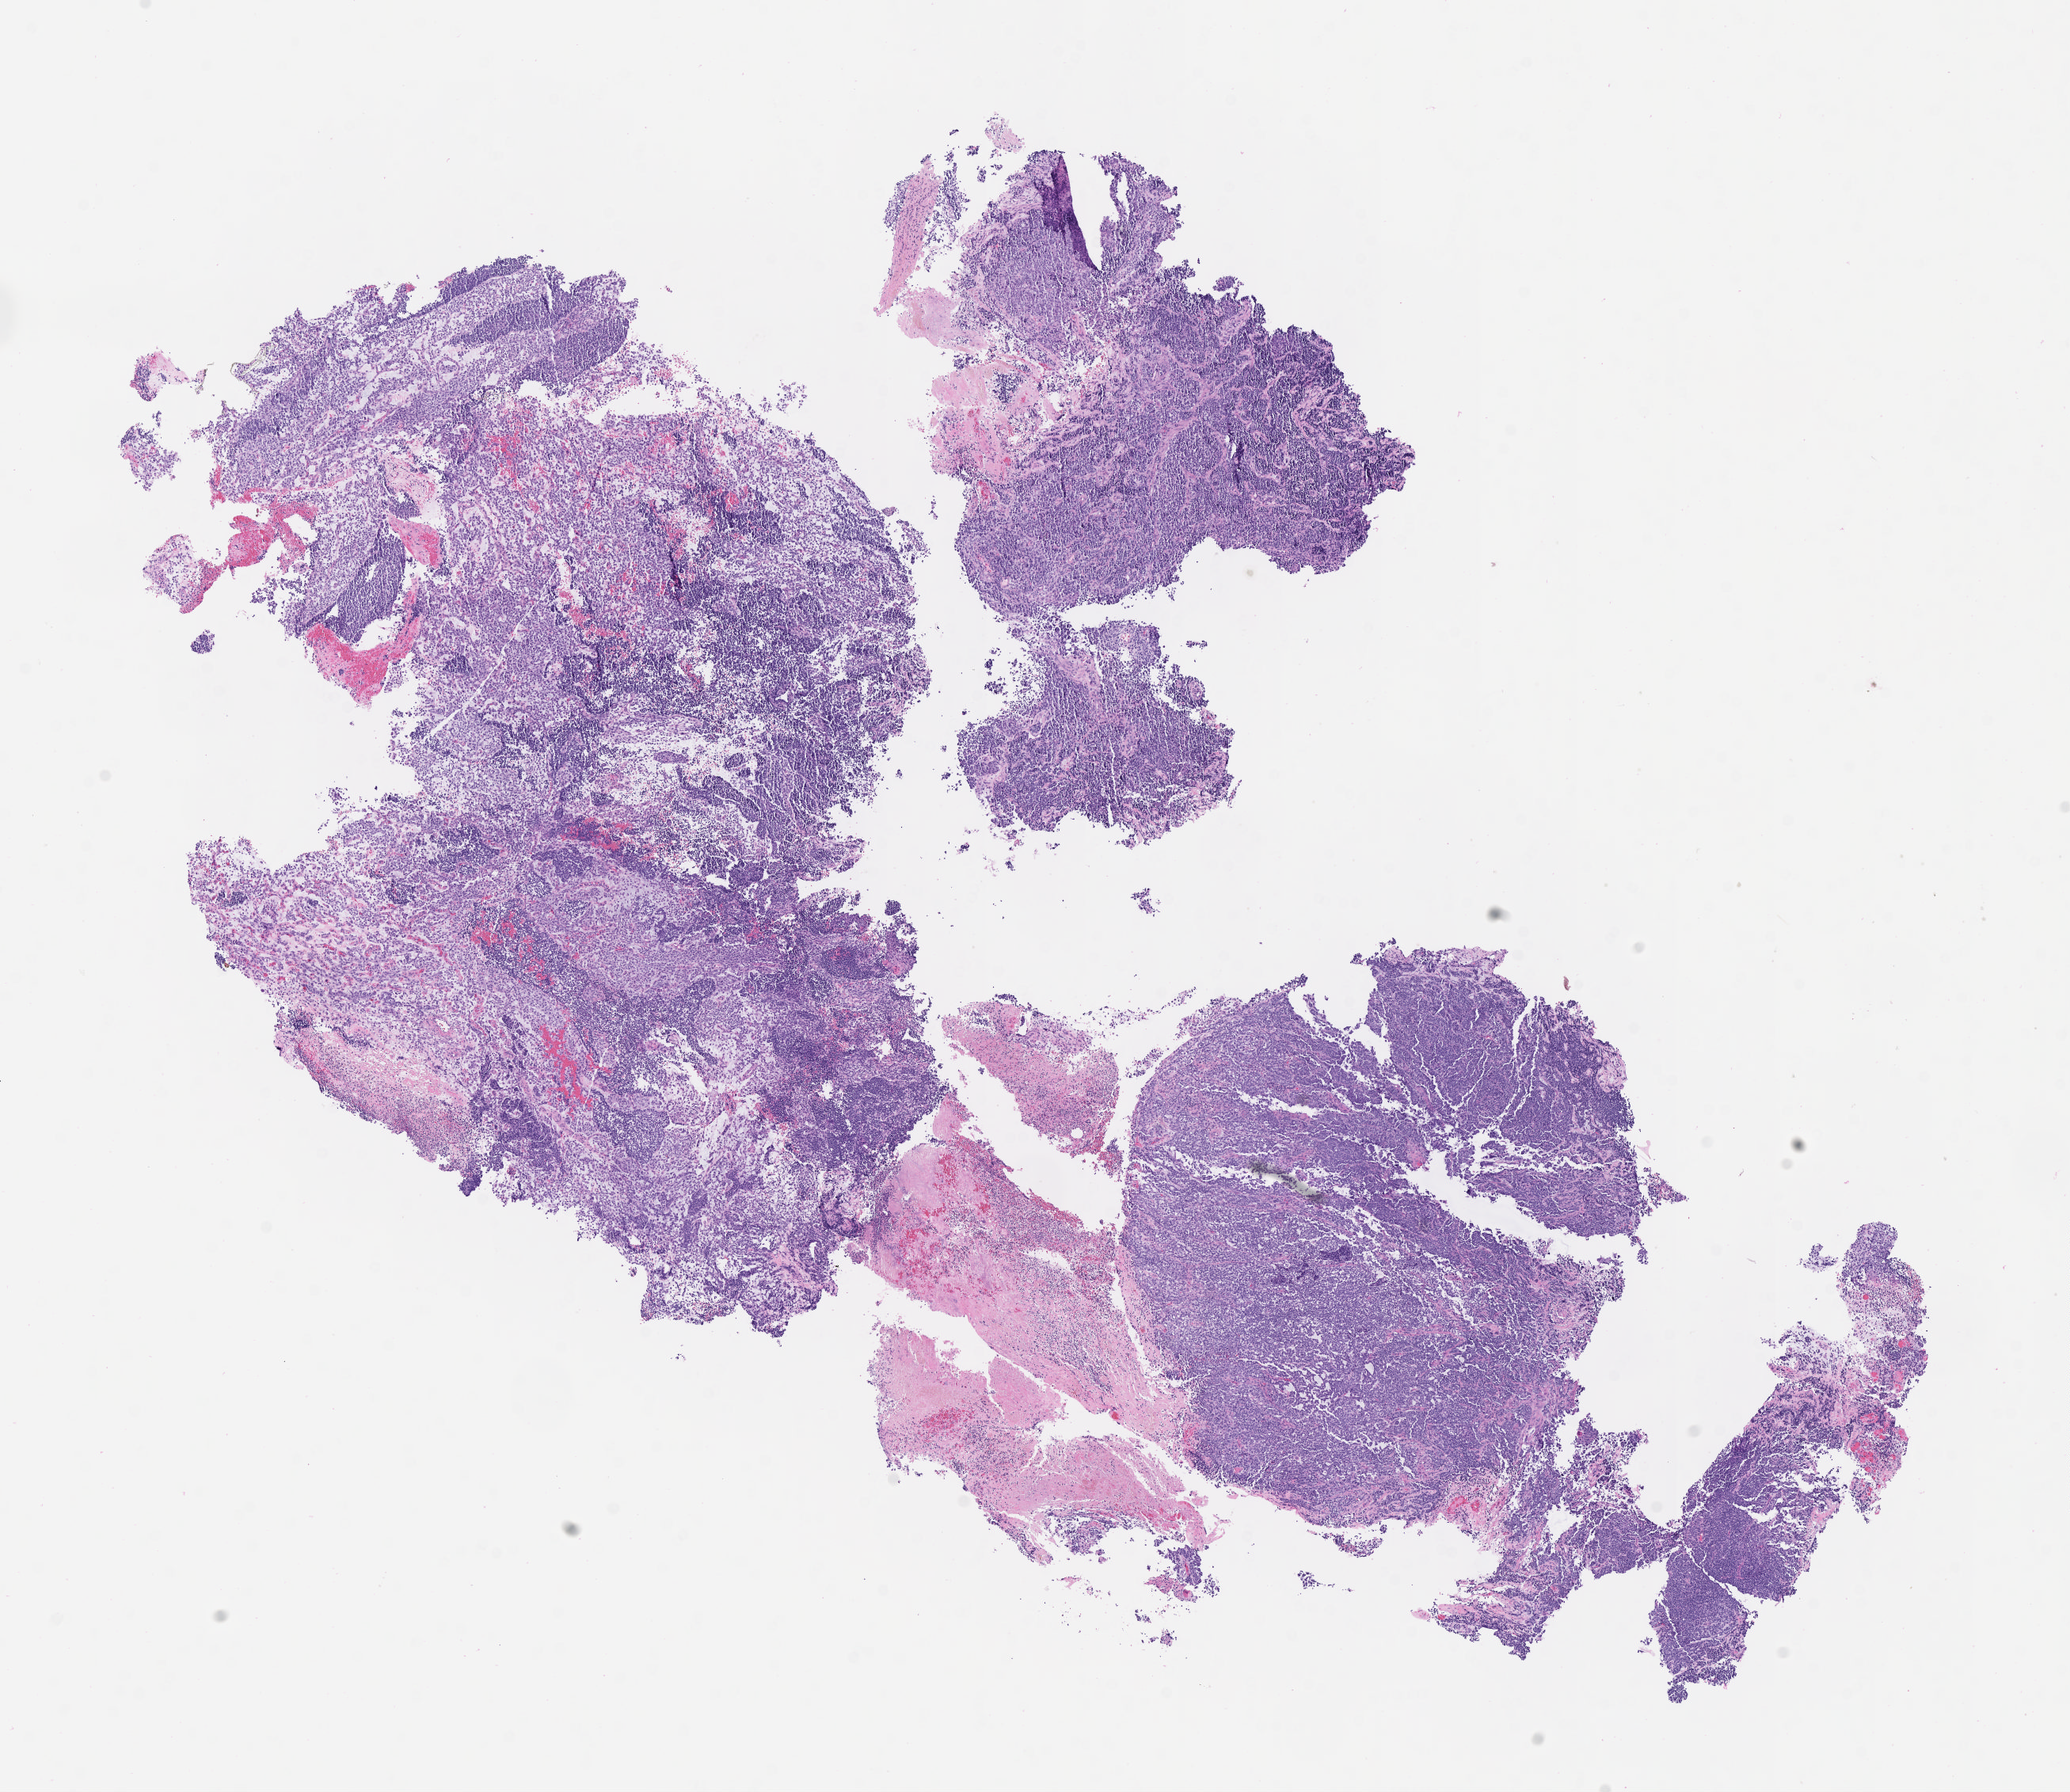
Whole-slide image, haematoxylin and eosin stain, shown as a low-resolution overview of the whole scanned area (about 10.6 x 9.1 mm), specimen: tumor tissue, site: cervix. Patient female; aged 57.
- diagnosis: Adenosquamous carcinoma